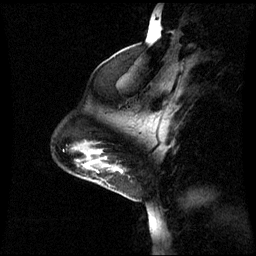
Breast MRI (dynamic contrast-enhanced), one sagittal slice; slice 14 of 60 in the series (ordered by position); dynamic contrast-enhanced series, image 2 of 3 at this slice position (ordered by acquisition); 1.5 T; TE 4.2 ms, TR 8.9 ms; 2.2 mm slice thickness; 256 × 256 image matrix. Female patient, age 44 years. Case-level facts recorded for this patient, not image findings: setting: breast cancer imaged before/during neoadjuvant chemotherapy; receptor status: triple-negative.
Structures marked on this image (semi-automatic segmentation, software-assisted and operator-edited):
- analysis volume of interest (the breast-tissue region the enhancement analysis was run in; not a lesion): box from (x=76, y=150) to (x=123, y=185) px
- tumour enhancement mask (voxels above the 70 % enhancement threshold inside the analysis volume of interest): (x=86, y=164)–(x=121, y=171)